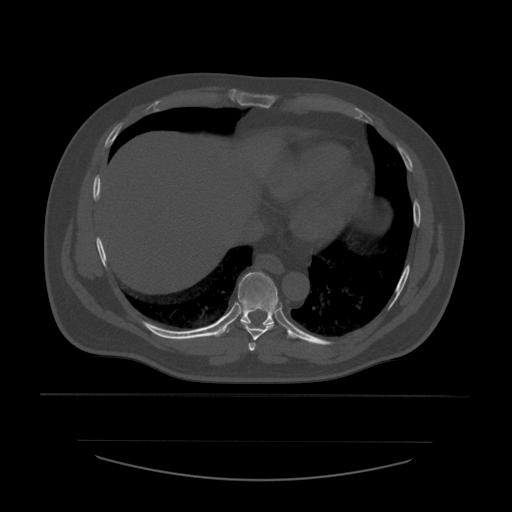
CT including the spine, one axial slice; reconstruction kernel STANDARD; 120 kVp; bone window (W 1800 / L 400 HU); 512 × 512 image matrix. Patient age 44 years. From the clinical record (not read from this slice): primary cancer: soft tissue sarcoma.
Structures marked on this image (semi-automatically segmented with operator editing):
- T7 vertebra: bounding box [x1, y1, x2, y2] px = [249, 343, 256, 353]
- T8 vertebra: [241, 322, 275, 341]
- T9 vertebra: [217, 272, 292, 338]